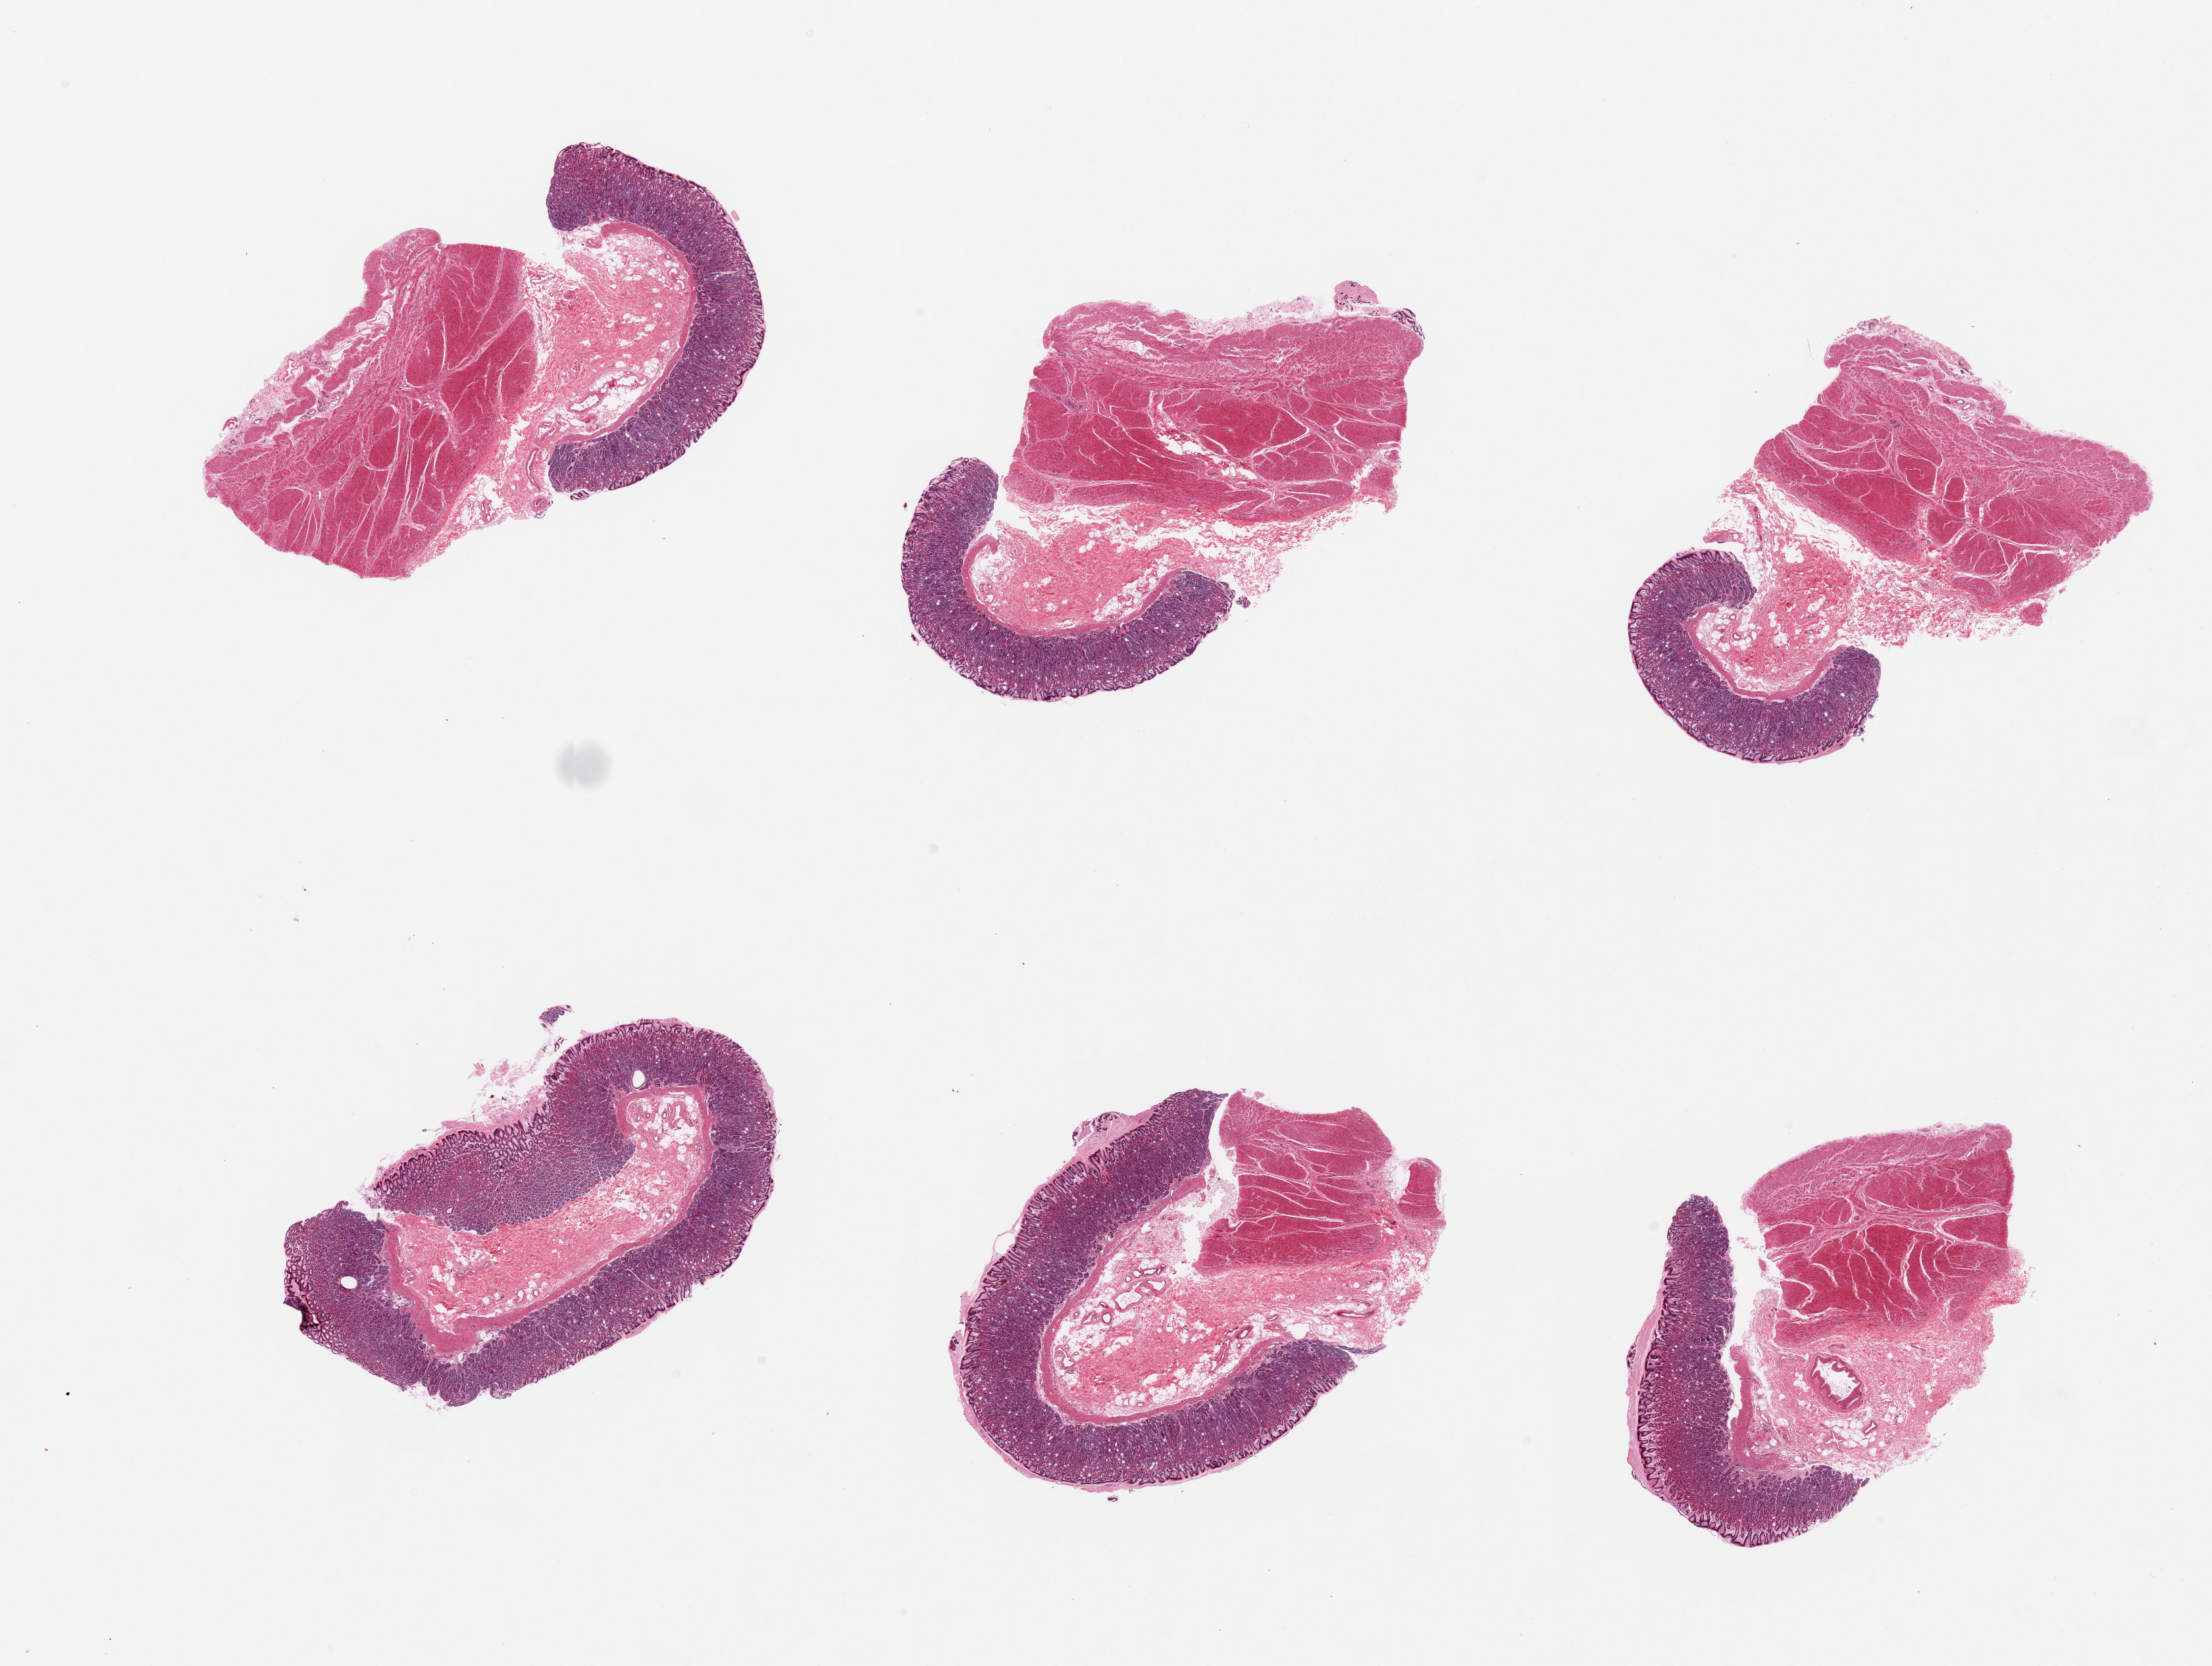
Haematoxylin and eosin whole-slide image, whole scanned area (about 26.6 x 20.0 mm) shown as a low-resolution overview, PAXgene-fixed, paraffin-embedded tissue, section of stomach (target tissue), donor tissue sample. Male donor.
* pathologist's review note for this sample: 6 pieces, well preserved mucosa and muscularis